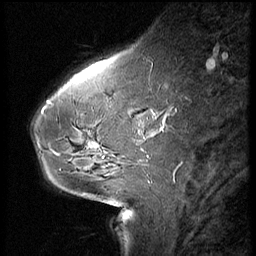
Breast MRI (dynamic contrast-enhanced), one sagittal slice. Slice 20 of 66 in the series (ordered by position). 3 images stored at this slice position (order not interpretable as contrast timing). 1.5 T. TE 4.2 ms, TR 8.9 ms. 2.5 mm slice thickness. 256 × 256 image matrix, field of view 200 × 200 mm. Patient: female, 54 years. Case-level facts recorded for this patient, not image findings: setting: breast cancer imaged before/during neoadjuvant chemotherapy; receptor status: HR-positive, HER2-negative.
Structures marked on this image (semi-automatically segmented with operator editing):
- analysis volume of interest (the breast-tissue region the enhancement analysis was run in; not a lesion): bounding box (x1, y1, x2, y2) in pixels: (61, 104, 146, 171)
- tumour enhancement mask (voxels above the 140 % enhancement threshold inside the analysis volume of interest): (134, 126, 145, 165)